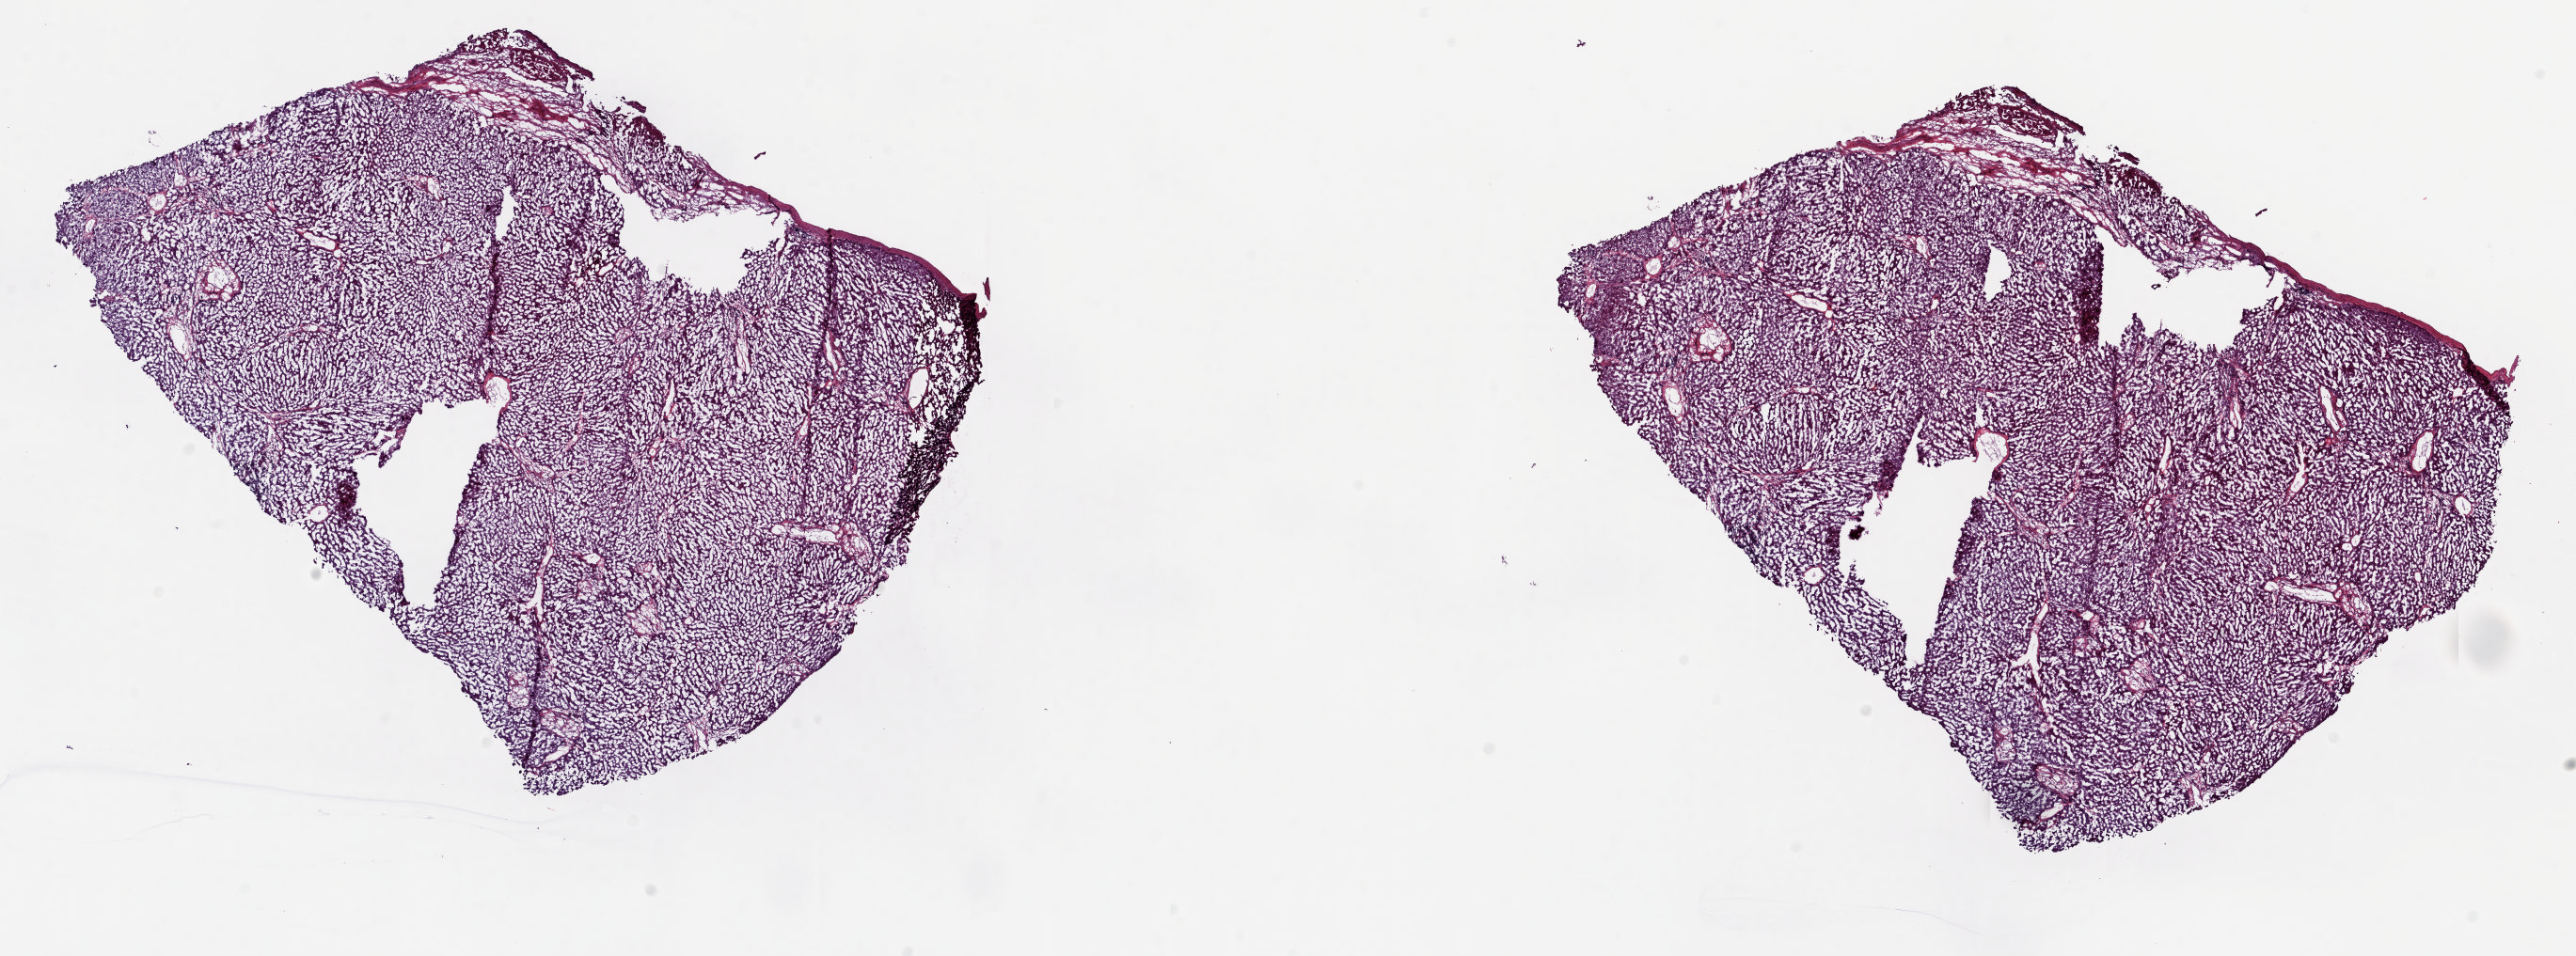
H&E-stained whole-slide image — a low-resolution overview of the entire scanned area, about 21.8 x 8.1 mm (acquisition: 20x scan). Frozen section. Solid tissue normal (non-tumour tissue) sample from the liver. Male patient; age at initial diagnosis 68 years. Slide review estimates, as recorded: tumour cells 0%, tumour nuclei 0%, normal cells 90%, stromal cells 10%, necrosis 0%. Inflammatory infiltration, as recorded: lymphocyte infiltration 1%, monocyte infiltration 0%, neutrophil infiltration 0%.
* this section: solid tissue normal (non-tumour) sample from the same patient
* patient diagnosis: Hepatocellular carcinoma, NOS